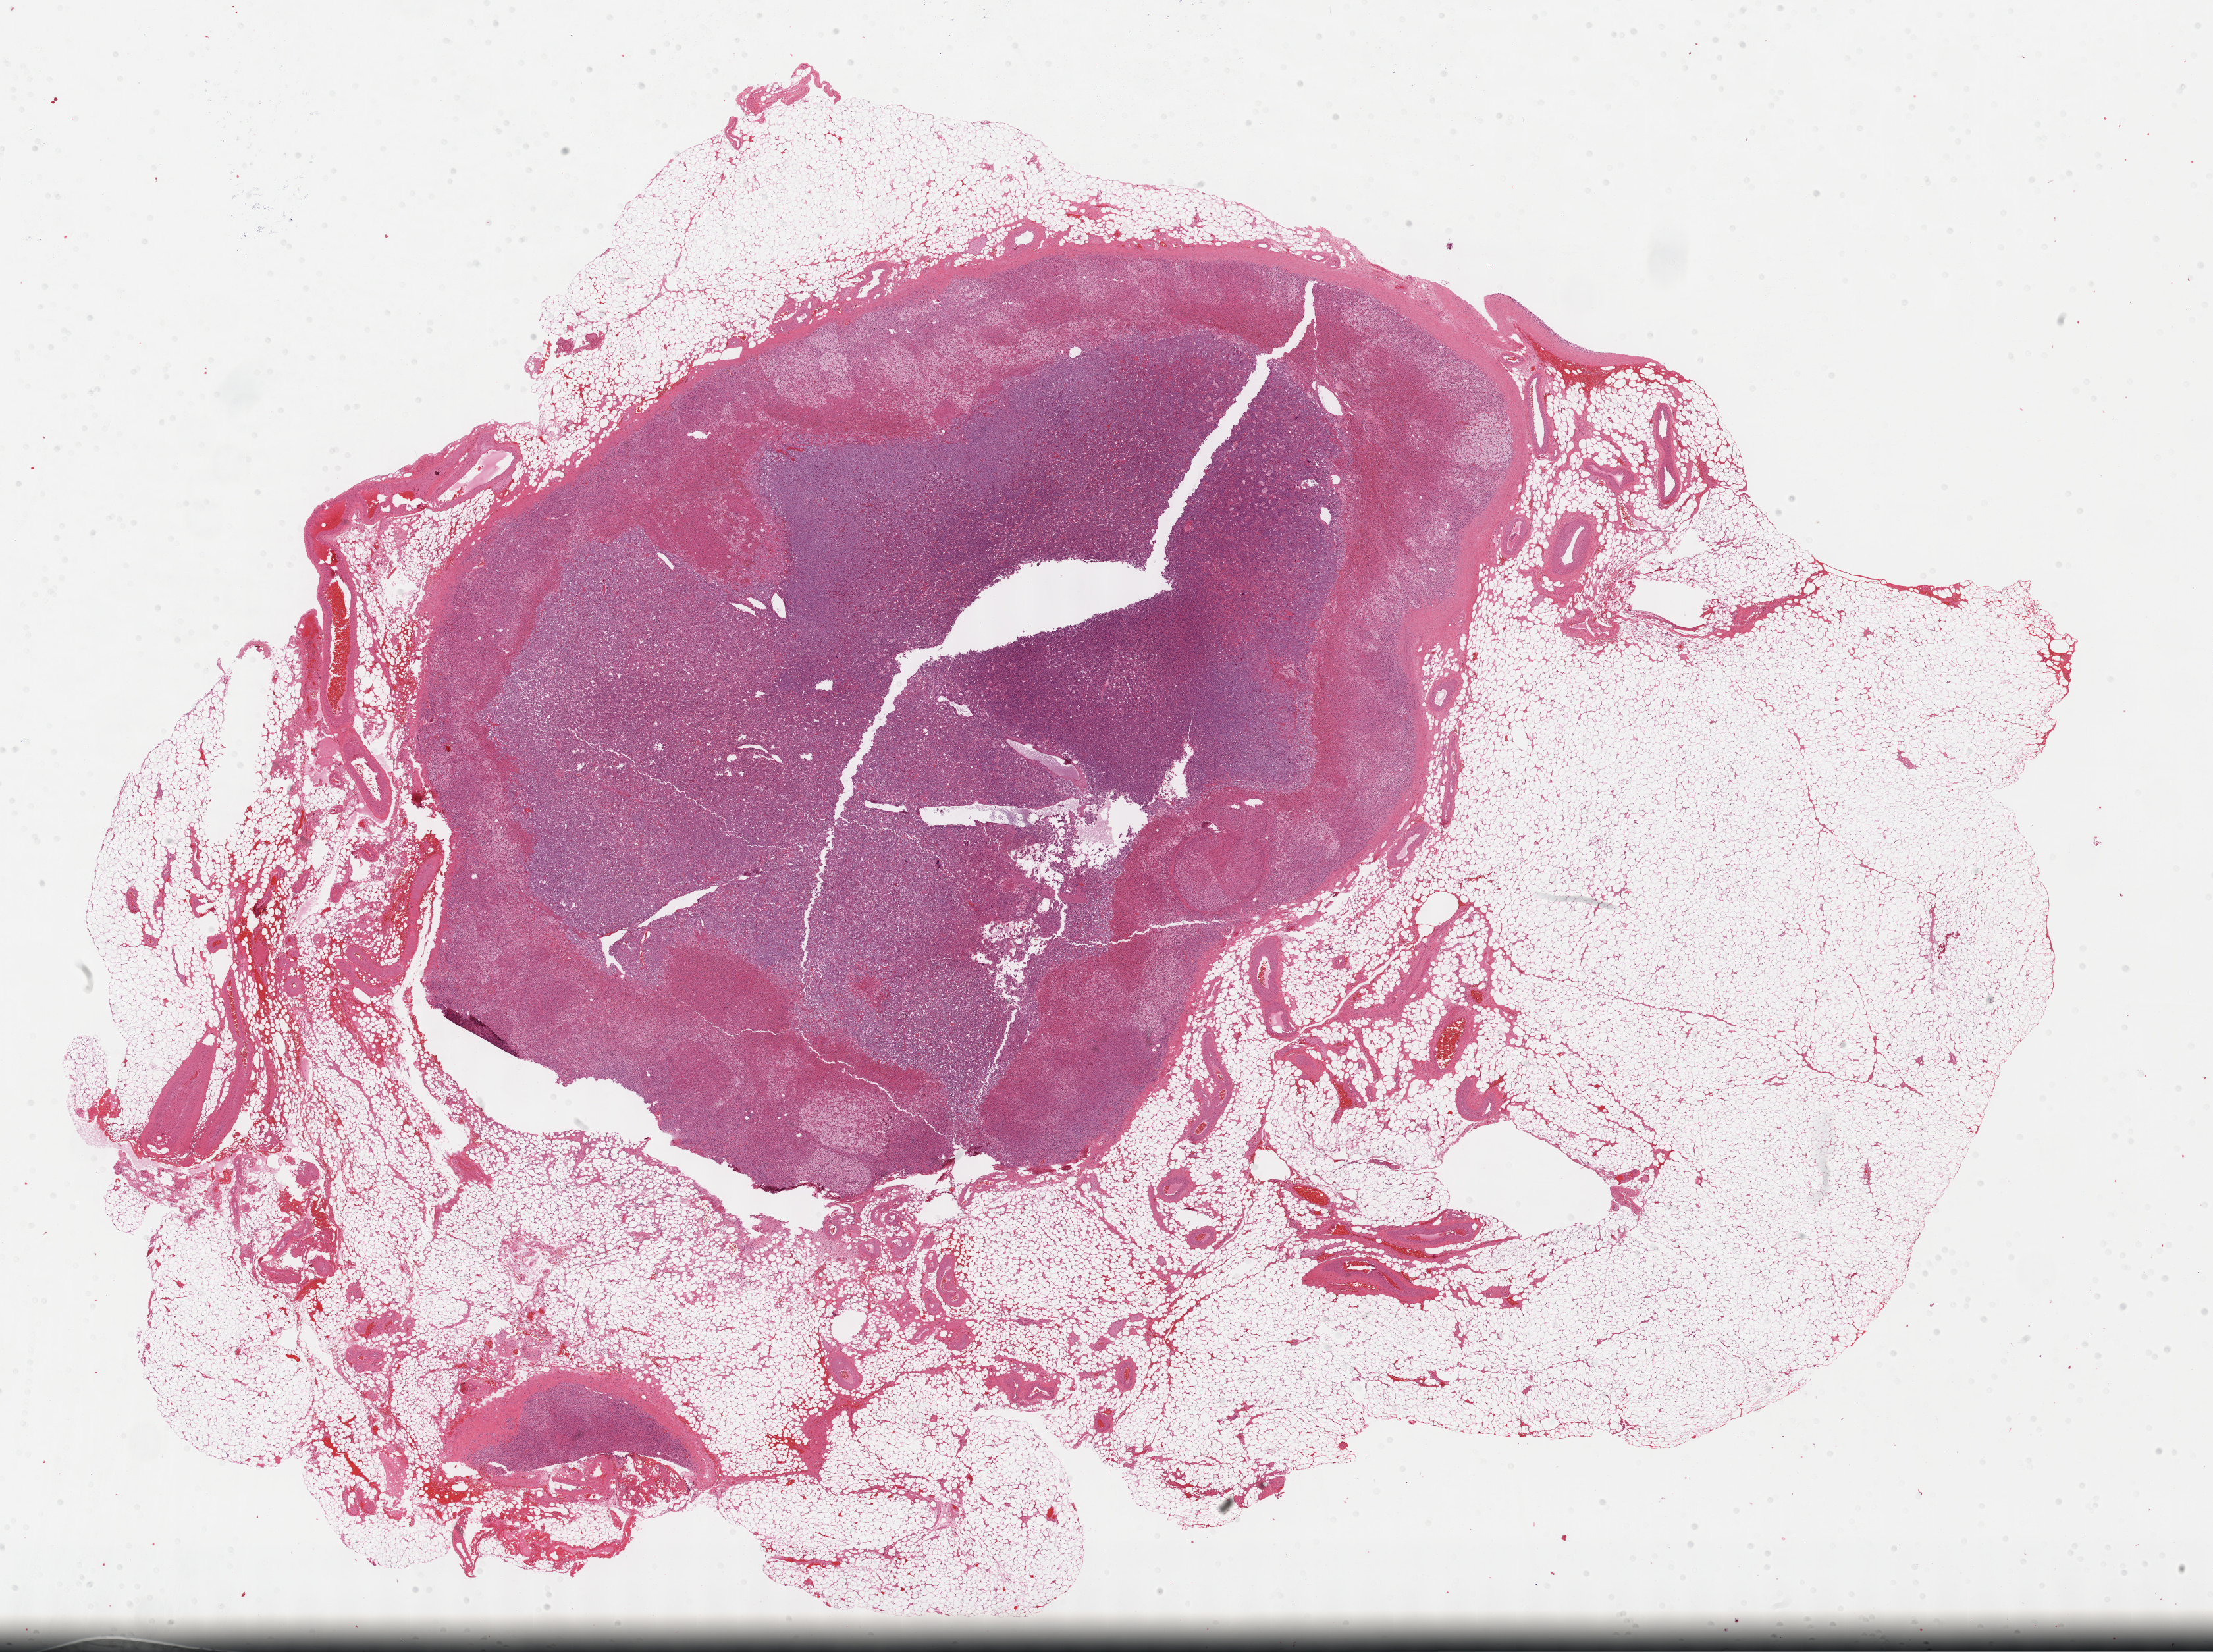
H&E whole-slide image, whole scanned area (about 27.2 x 20.3 mm, from a 40x scan) shown as a low-resolution overview. Formalin-fixed paraffin-embedded (FFPE) diagnostic section. Adrenal gland, primary tumour sample. Patient: male, age at initial diagnosis 80 years.
* diagnosis: Pheochromocytoma, NOS